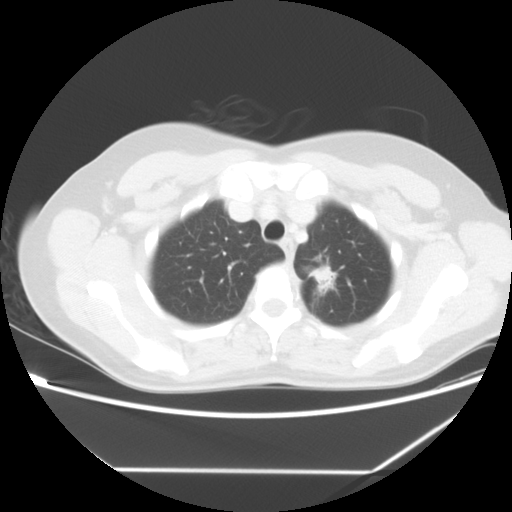
Chest CT, one axial slice; slice 49 of 60 in the series (ordered by position); reconstruction kernel STANDARD; 140 kVp; lung window (W 1500 / L -600 HU); 5 mm slice thickness; 512 × 512 image matrix, field of view 367 × 367 mm. Female patient, age 43 years. From the clinical record (not read from this slice): clinical TNM (as recorded): T1c N0 M1b.
Annotated regions visible in this slice (rectangle marked by the reading radiologist):
- lung tumour (recorded histology: adenocarcinoma): box from (x=307, y=262) to (x=341, y=309) px